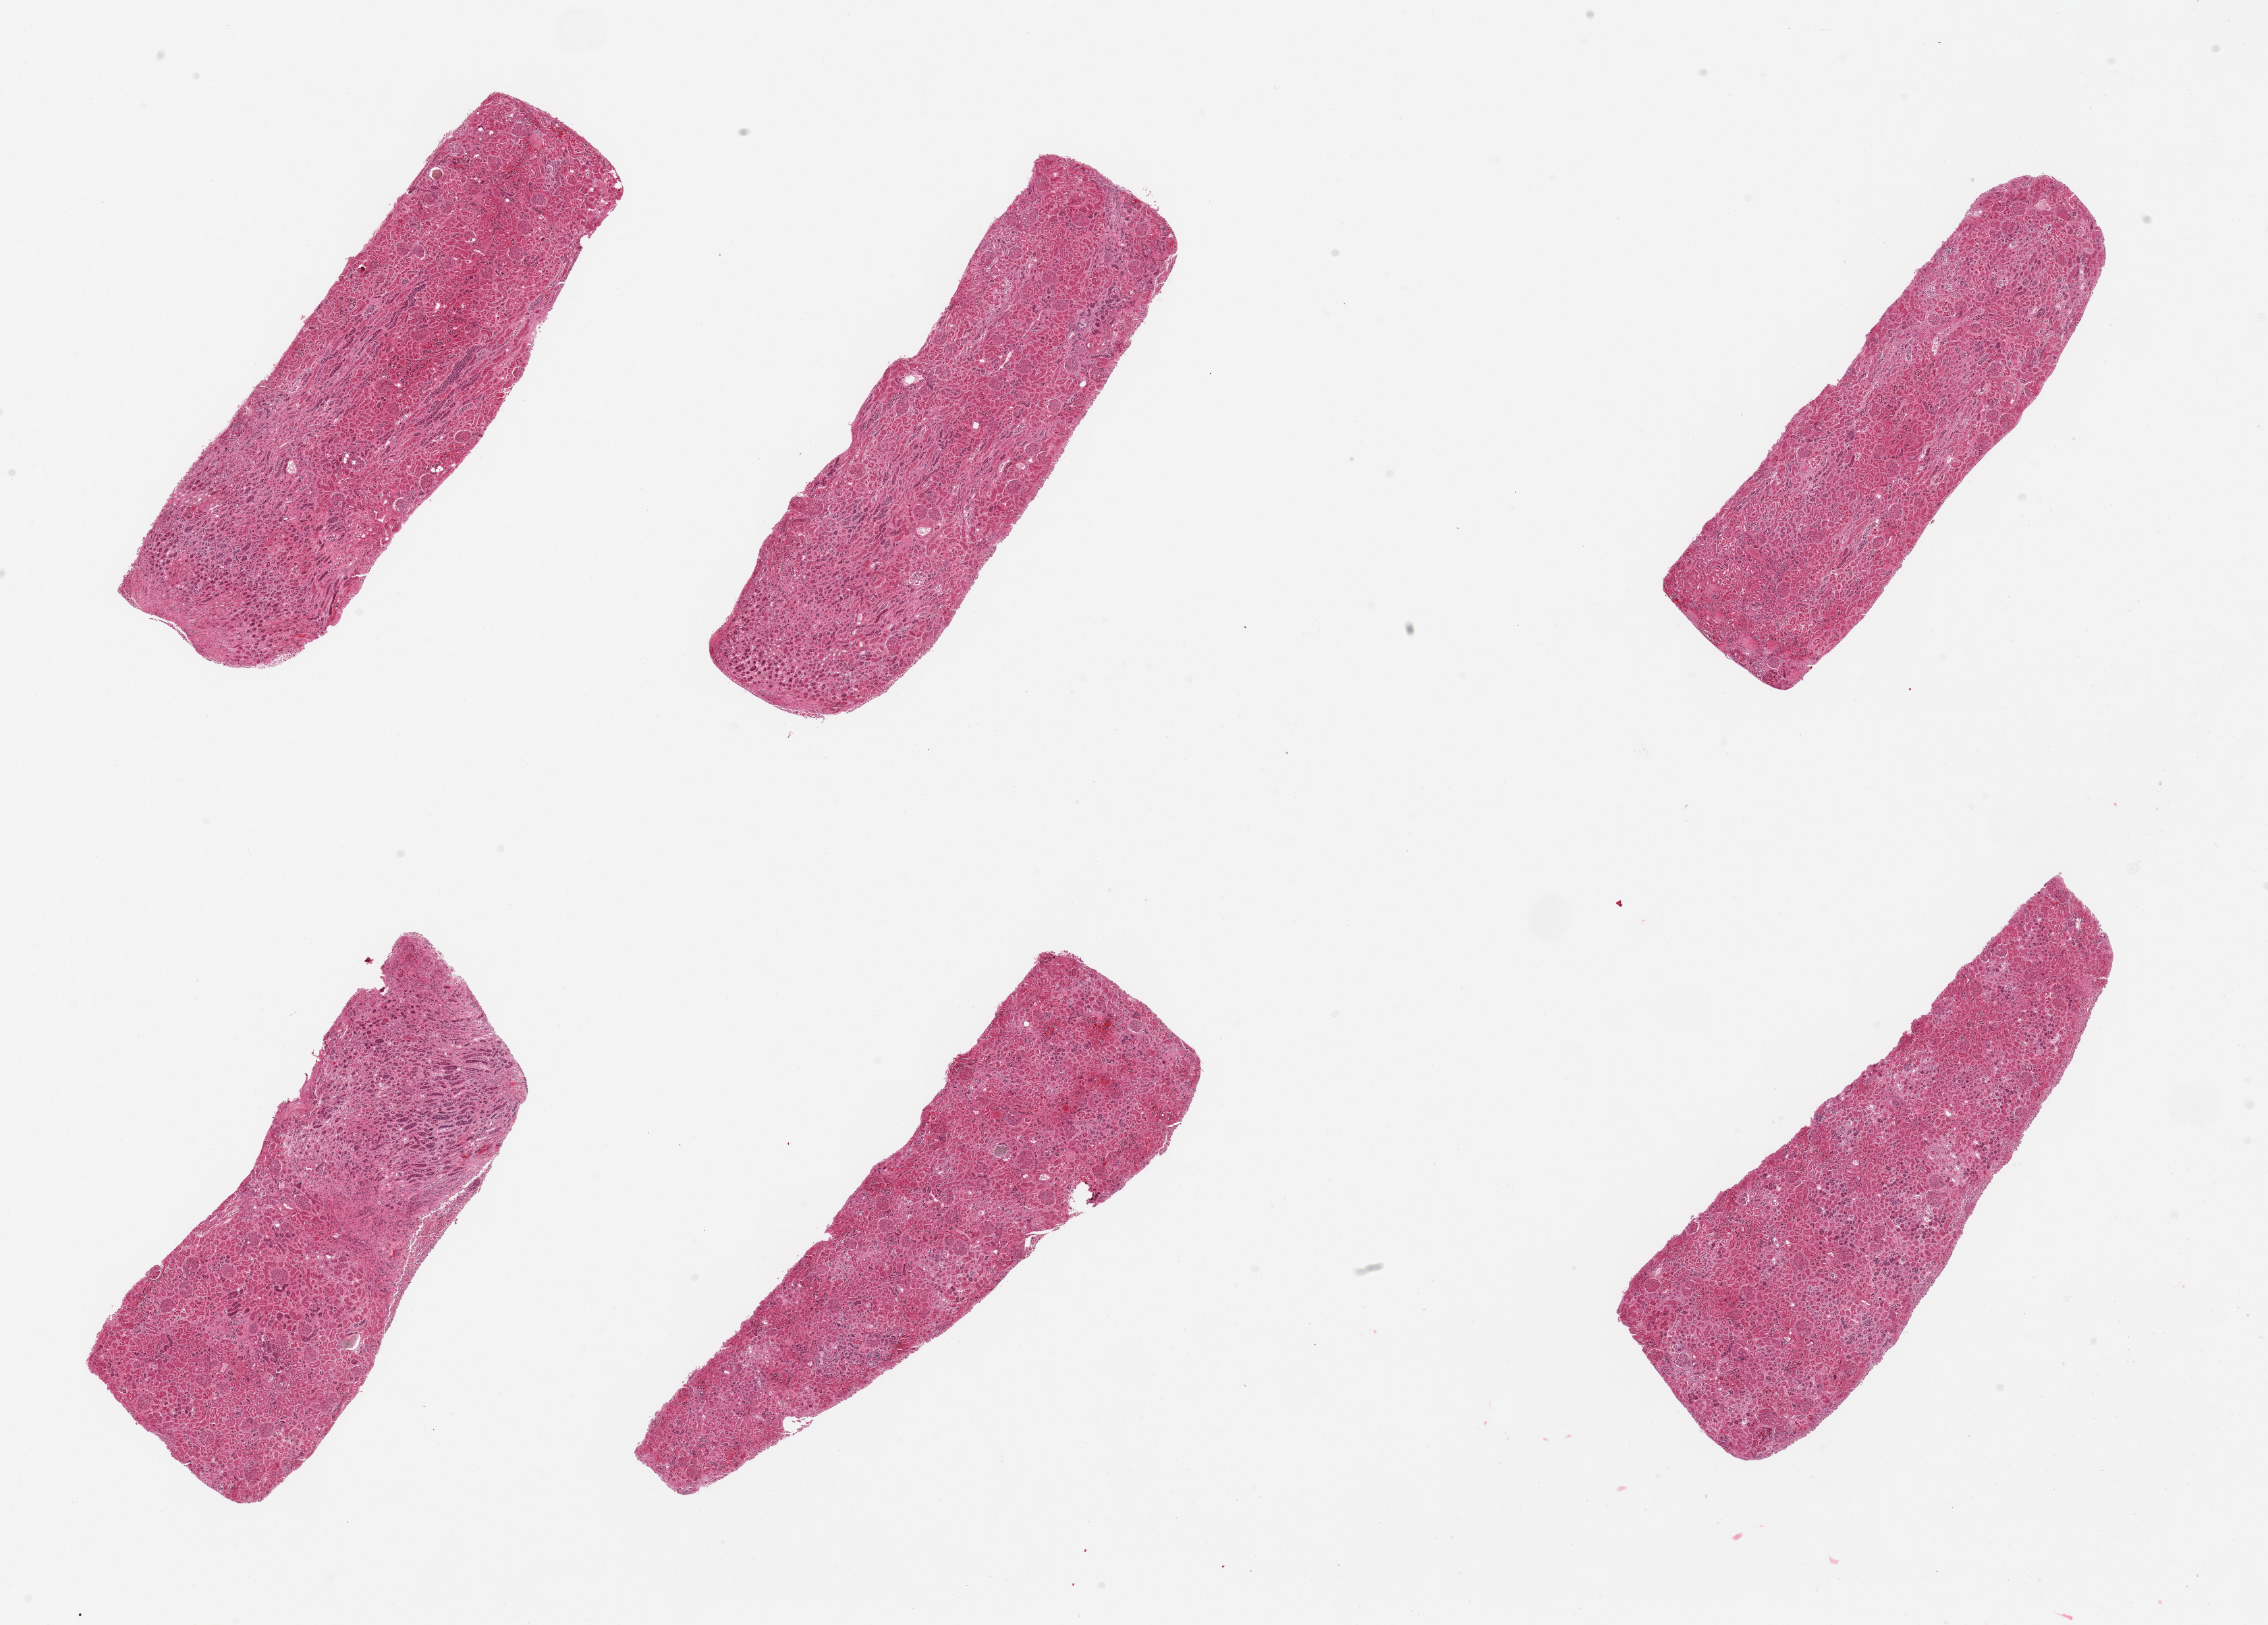
Haematoxylin and eosin whole-slide image — shown as a low-resolution overview of the whole scanned area (about 26.6 x 19.0 mm, slide scanned at 20x), PAXgene-fixed, paraffin-embedded tissue, section of renal cortex (target tissue), donor tissue sample. Donor: female.
* review note (as recorded): 6 pieces, glomeruli present, tubules autolyzed